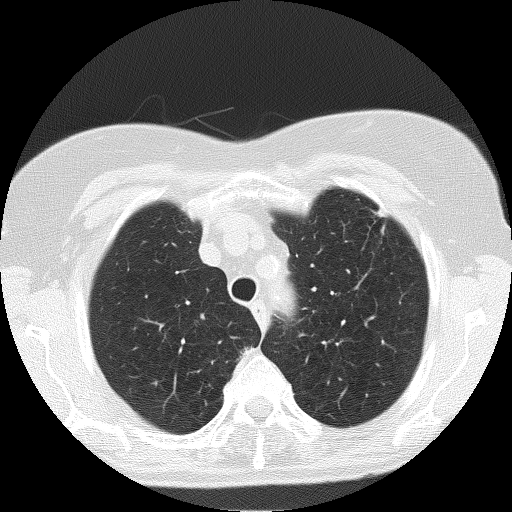
Low-dose screening chest CT, one axial slice. Reconstruction kernel FC51. Lung window (W 1500 / L -600 HU). 2 mm slice thickness. 512 × 512 image matrix, field of view 303 × 303 mm.
Structures marked on this image (expert manual segmentation):
- lesion 1 (tumor, upper lobe of left lung): box from (x=377, y=212) to (x=383, y=216) px